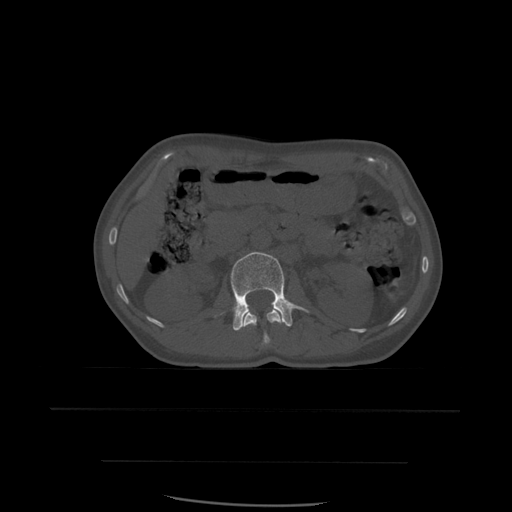
CT including the spine, one axial slice; slice 233 of 574 in the series (ordered by position); bone window (W 1800 / L 400 HU); 512 × 512 image matrix. Patient age 48 years. Case-level facts recorded for this patient, not image findings: primary cancer: lung; vertebrae with lytic lesions (as recorded): T11.
Outlined on this slice (semi-automatic segmentation, software-assisted and operator-edited):
- L1 vertebra: bounding box <242,309,284,346> (left, top, right, bottom; pixels)
- L2 vertebra: <231,252,309,331>